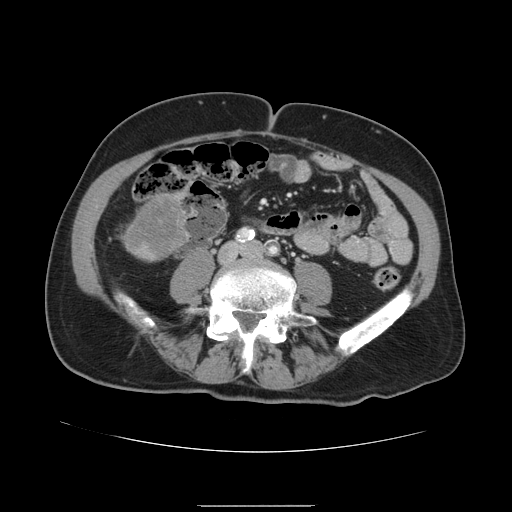
Contrast-enhanced abdominal CT, one axial slice; position 11 of 168 along the scan axis; 120 kVp; soft-tissue window (W 400 / L 40 HU); 2.5 mm slice thickness; 512 × 512 image matrix, field of view 386 × 386 mm. Male patient, age 74 years. Case-level facts recorded for this patient, not image findings: diagnosis: colorectal cancer liver metastases, imaged before liver resection; multiple liver metastases: no; largest metastasis: 14.5 cm; disease in both lobes: yes.
Annotated regions visible in this slice (expert manual segmentation):
- liver: bounding box <124,193,189,263> (left, top, right, bottom; pixels)
- liver metastasis: <127,196,185,257>